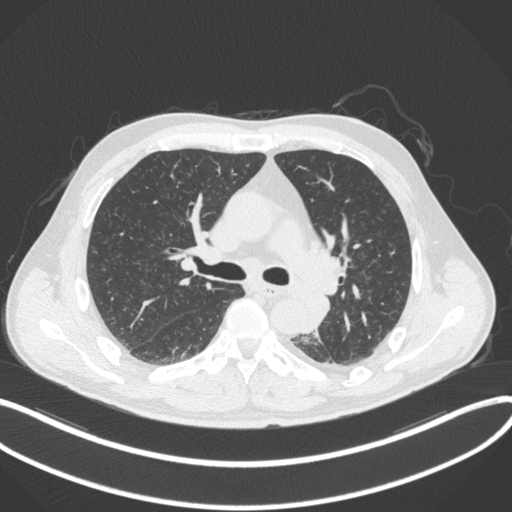
Chest CT, one axial slice; slice 215 of 328 in the series (ordered by position); reconstruction kernel B31f; lung window (W 1500 / L -600 HU); 1 mm slice thickness; 512 × 512 image matrix, field of view 400 × 400 mm. Patient: male, 59 years. Case-level facts recorded for this patient, not image findings: clinical TNM (as recorded): T2a N2 M0.
Outlined on this slice (bounding box drawn by a radiologist):
- lung tumour (recorded histology: squamous cell carcinoma): box from (x=305, y=288) to (x=332, y=336) px